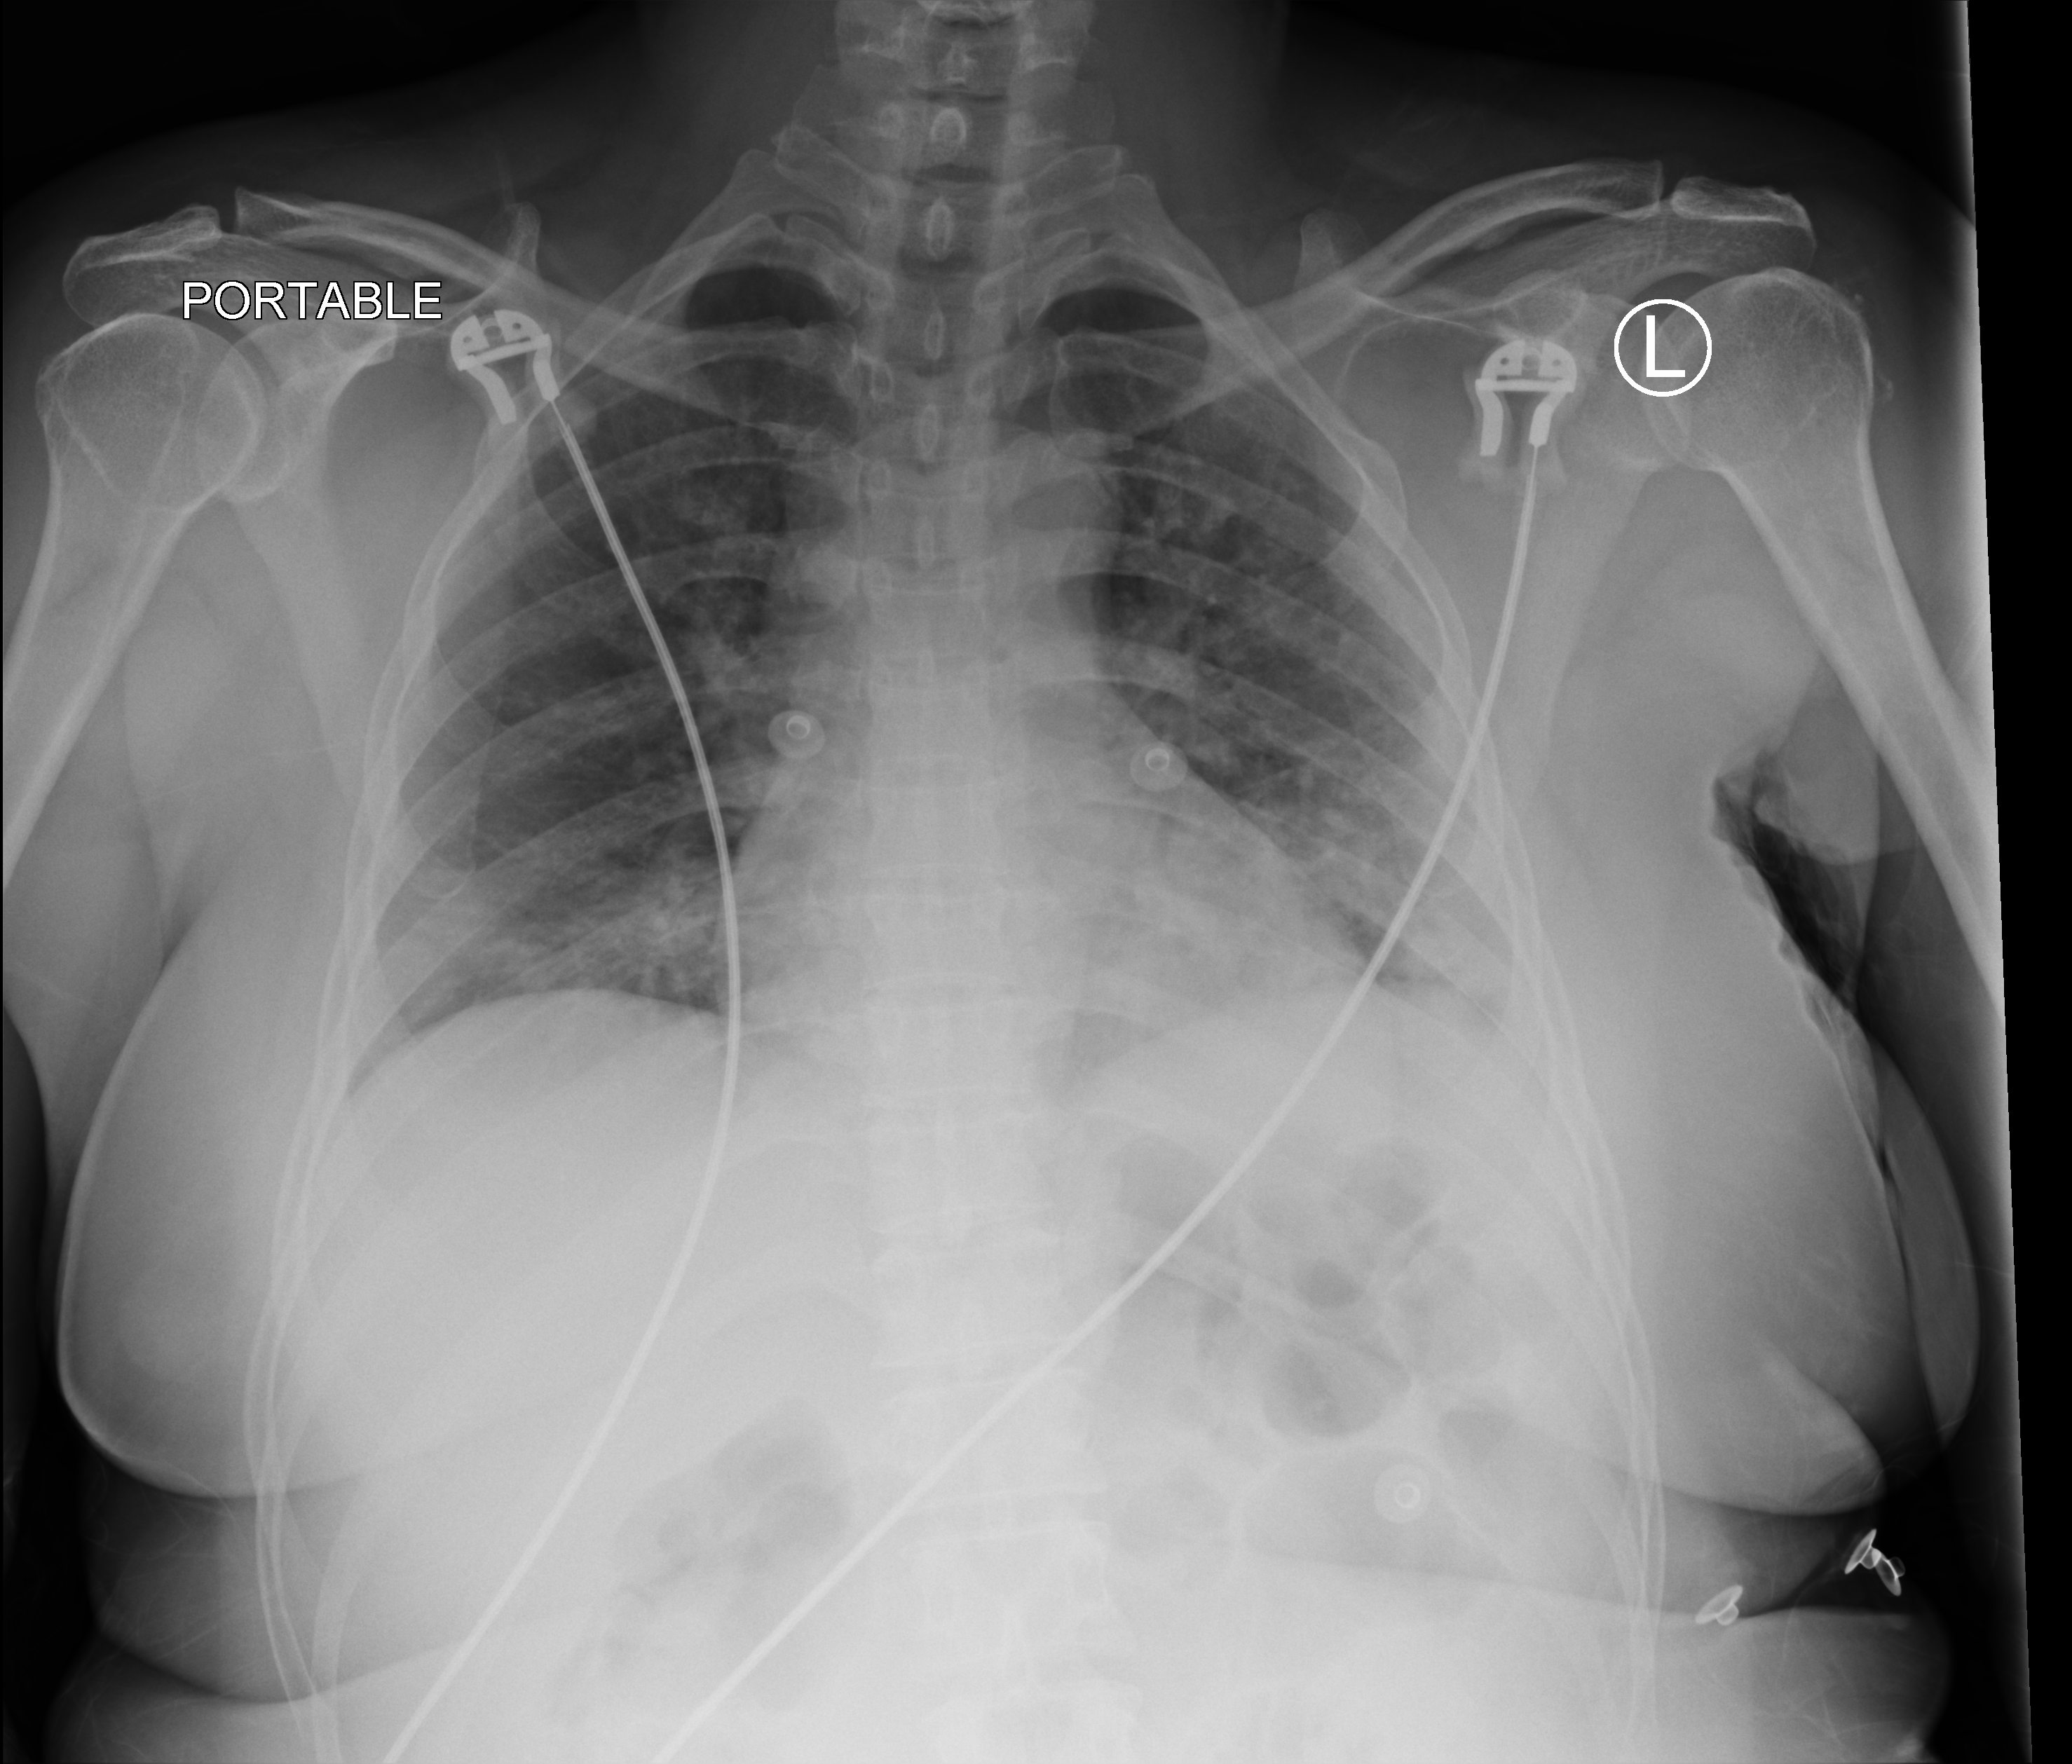
Chest X-ray (portable), anteroposterior (AP) projection. Female patient hospitalised with COVID-19, age 18–59 years.
Admission-level facts for this patient (not findings on this image; timing relative to this image not recorded):
- length of hospital stay: 1 day
- admitted to intensive care during this hospital stay: no
- mechanically ventilated during this hospital stay: no